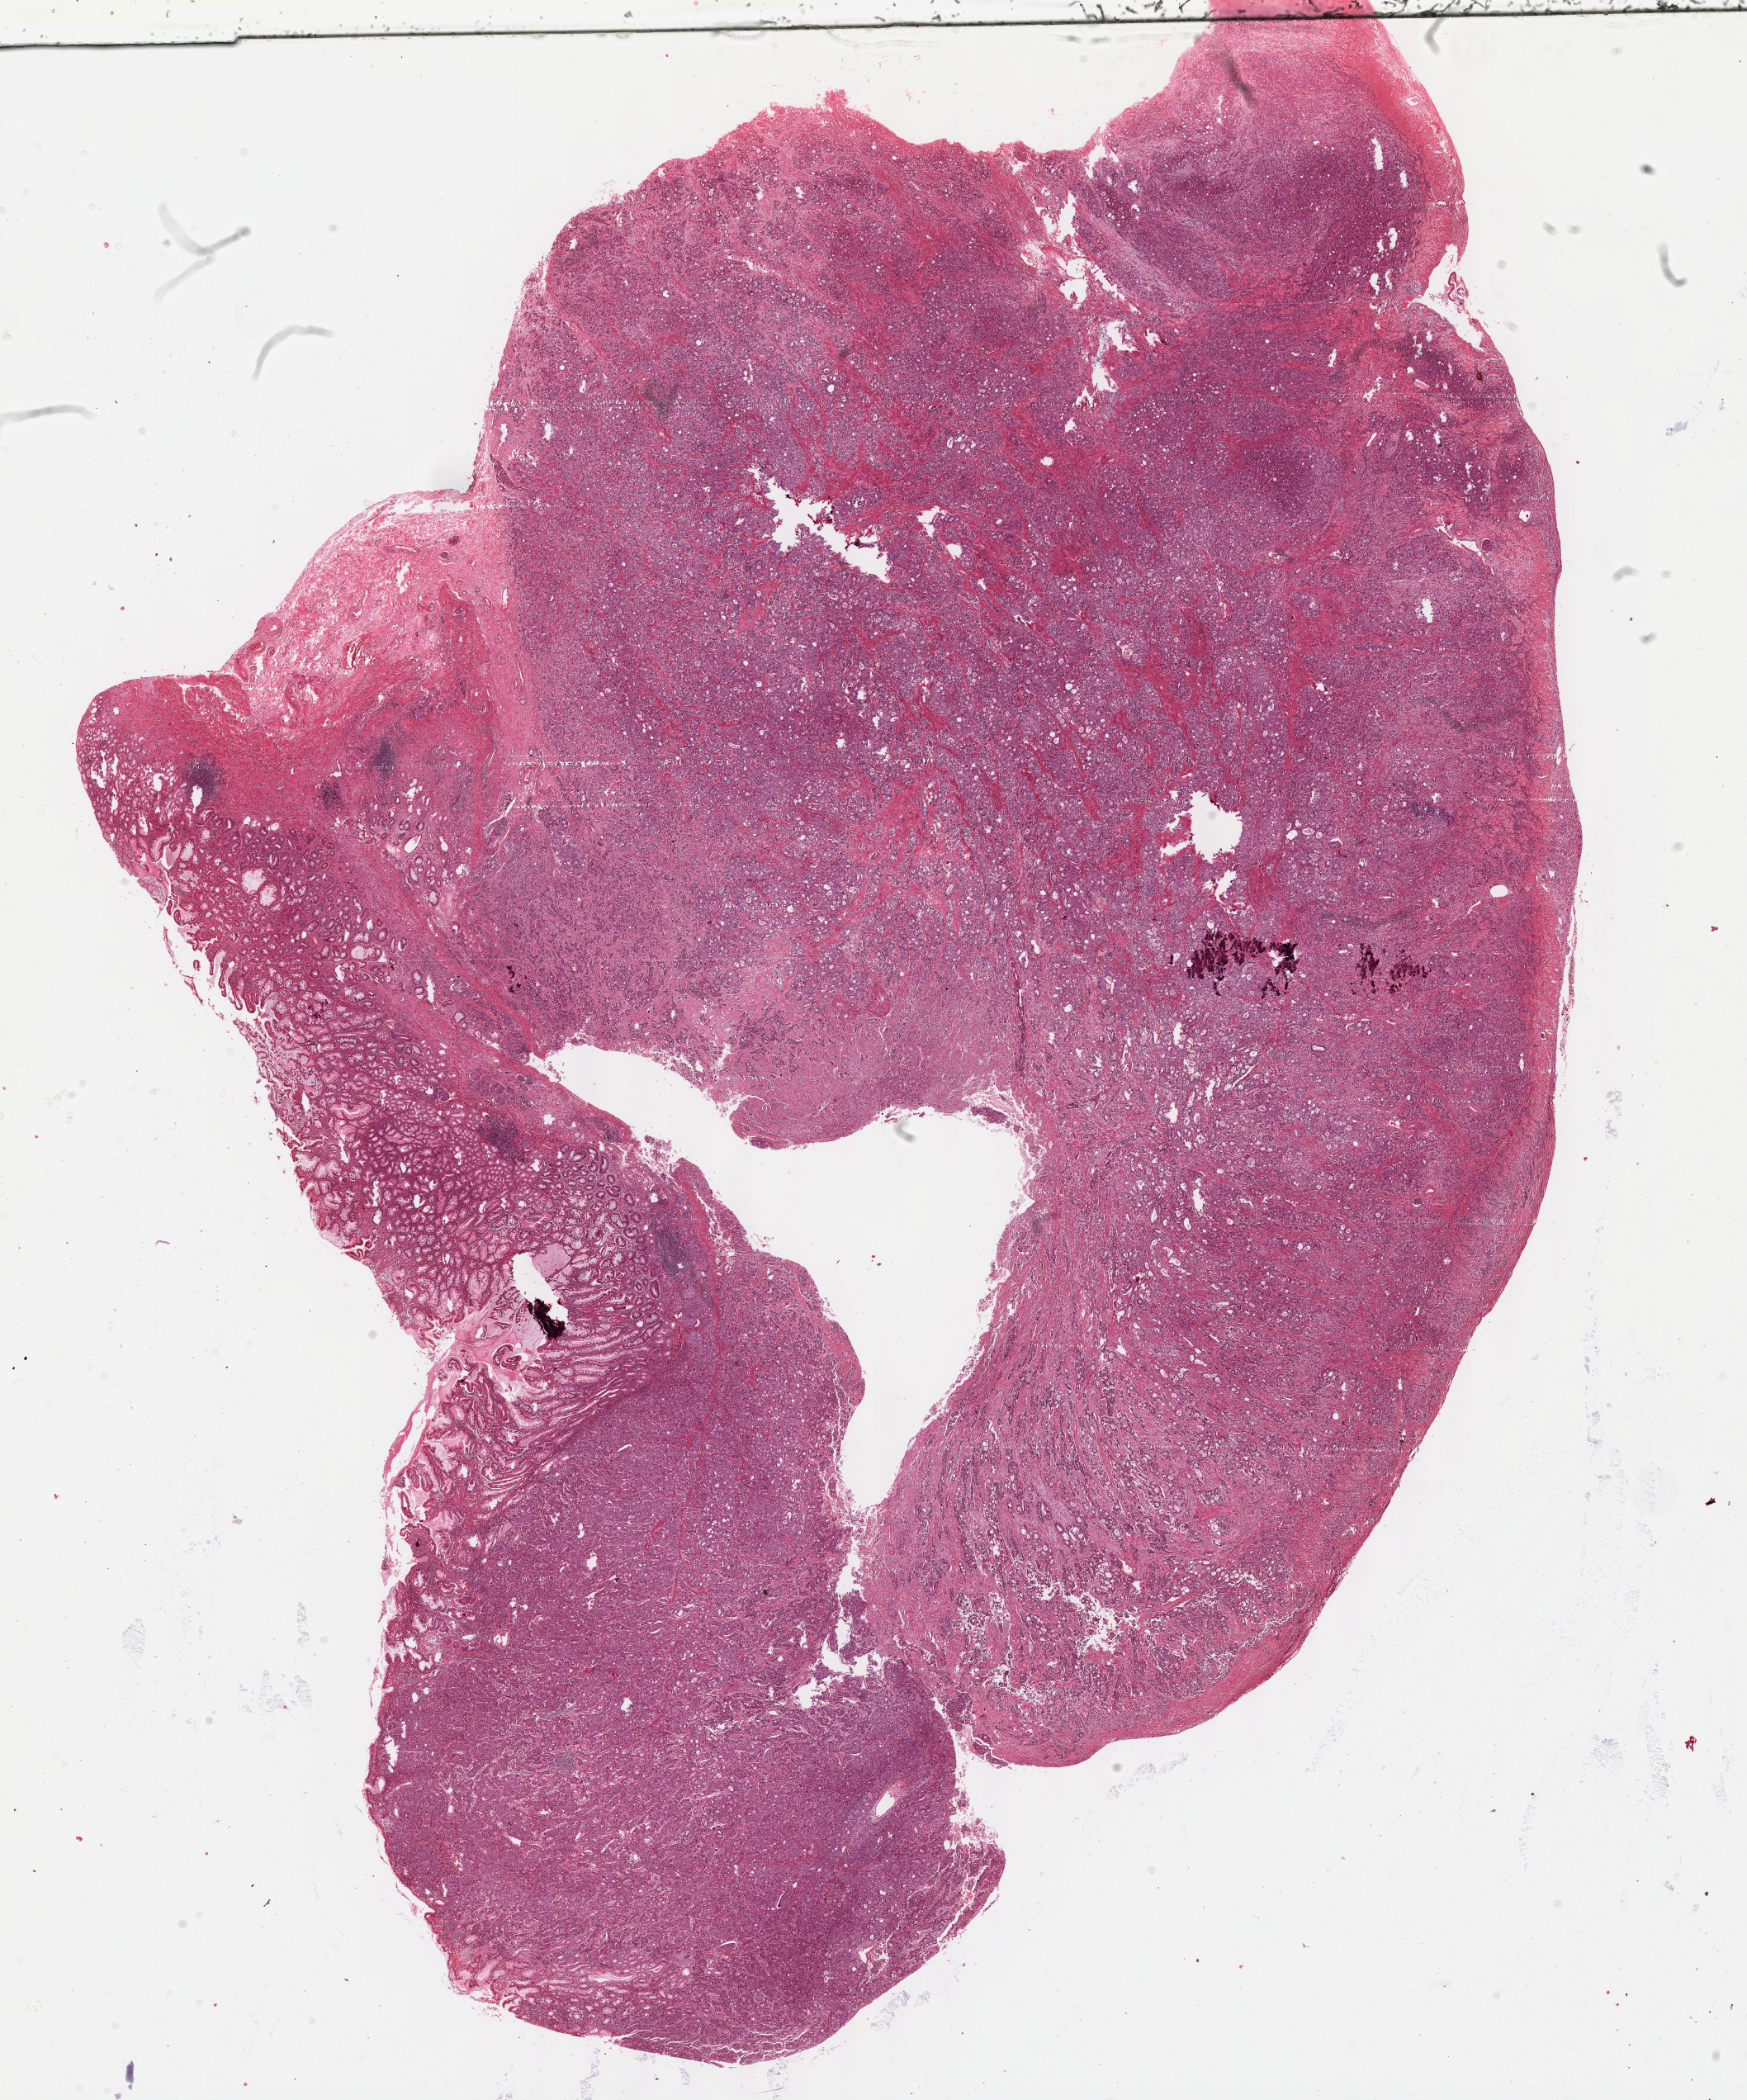
Whole-slide histology image, H&E-stained — low-resolution overview of the scanned area, about 17.1 x 20.6 mm (slide scanned at 40x); FFPE section; sample: primary tumour, stomach. Female patient; age at initial diagnosis 72 years. Histologic grade: G2 (moderately differentiated).
• AJCC pathologic stage: II (6th edition)
• pathologic diagnosis: Adenocarcinoma, intestinal type